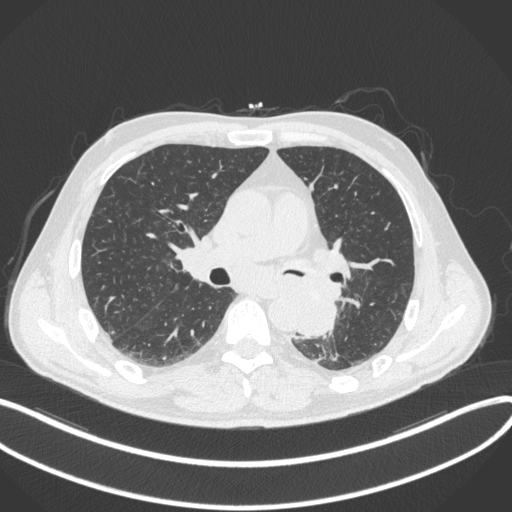
Chest CT, one axial slice; position 195 of 328 along the scan axis; lung window (W 1500 / L -600 HU); 1 mm slice thickness; 512 × 512 image matrix. Patient: male, 59 years. From the clinical record (not read from this slice): clinical TNM (as recorded): T2a N2 M0.
Outlined on this slice (bounding box drawn by a radiologist):
- lung tumour (recorded histology: squamous cell carcinoma): box from (x=295, y=288) to (x=341, y=340) px